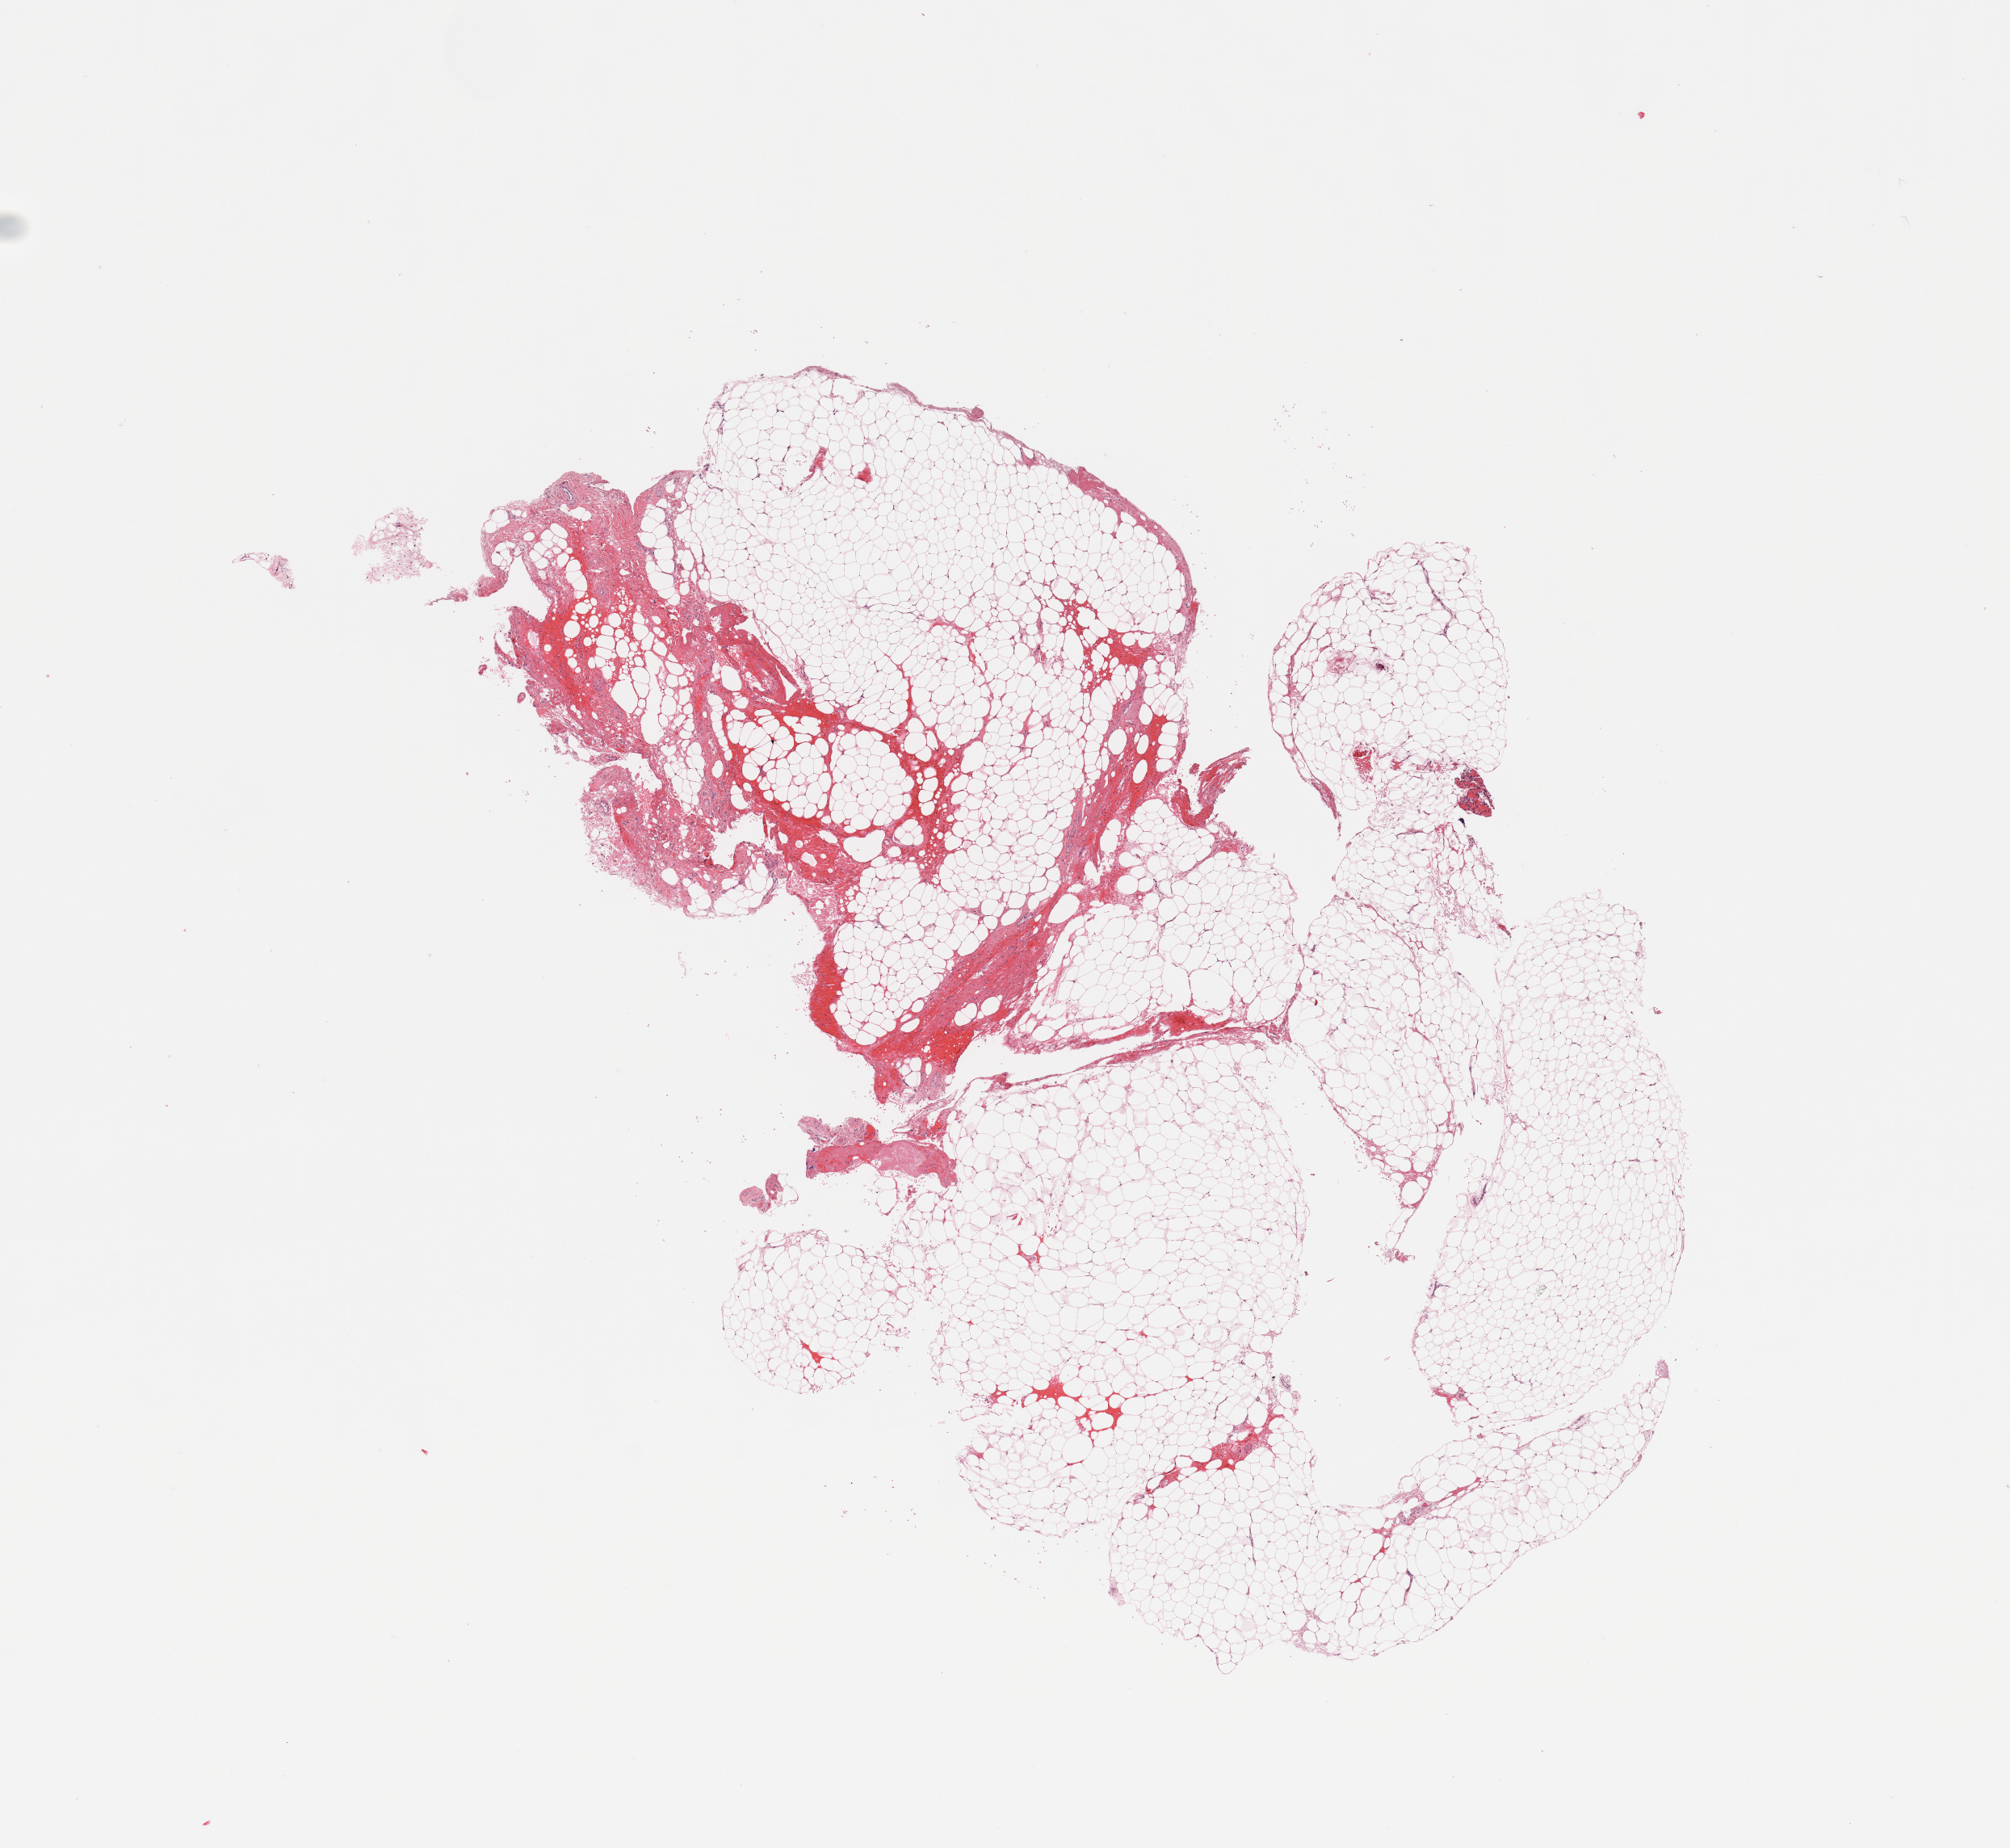
Digitized H&E tissue section (whole slide), a low-resolution overview of the entire scanned area, about 9.8 x 9.0 mm; kidney, normal (non-tumour) tissue. 31-year-old female patient.
This section: normal (non-tumour) tissue from the same patient. Patient diagnosis: Renal cell carcinoma, NOS.